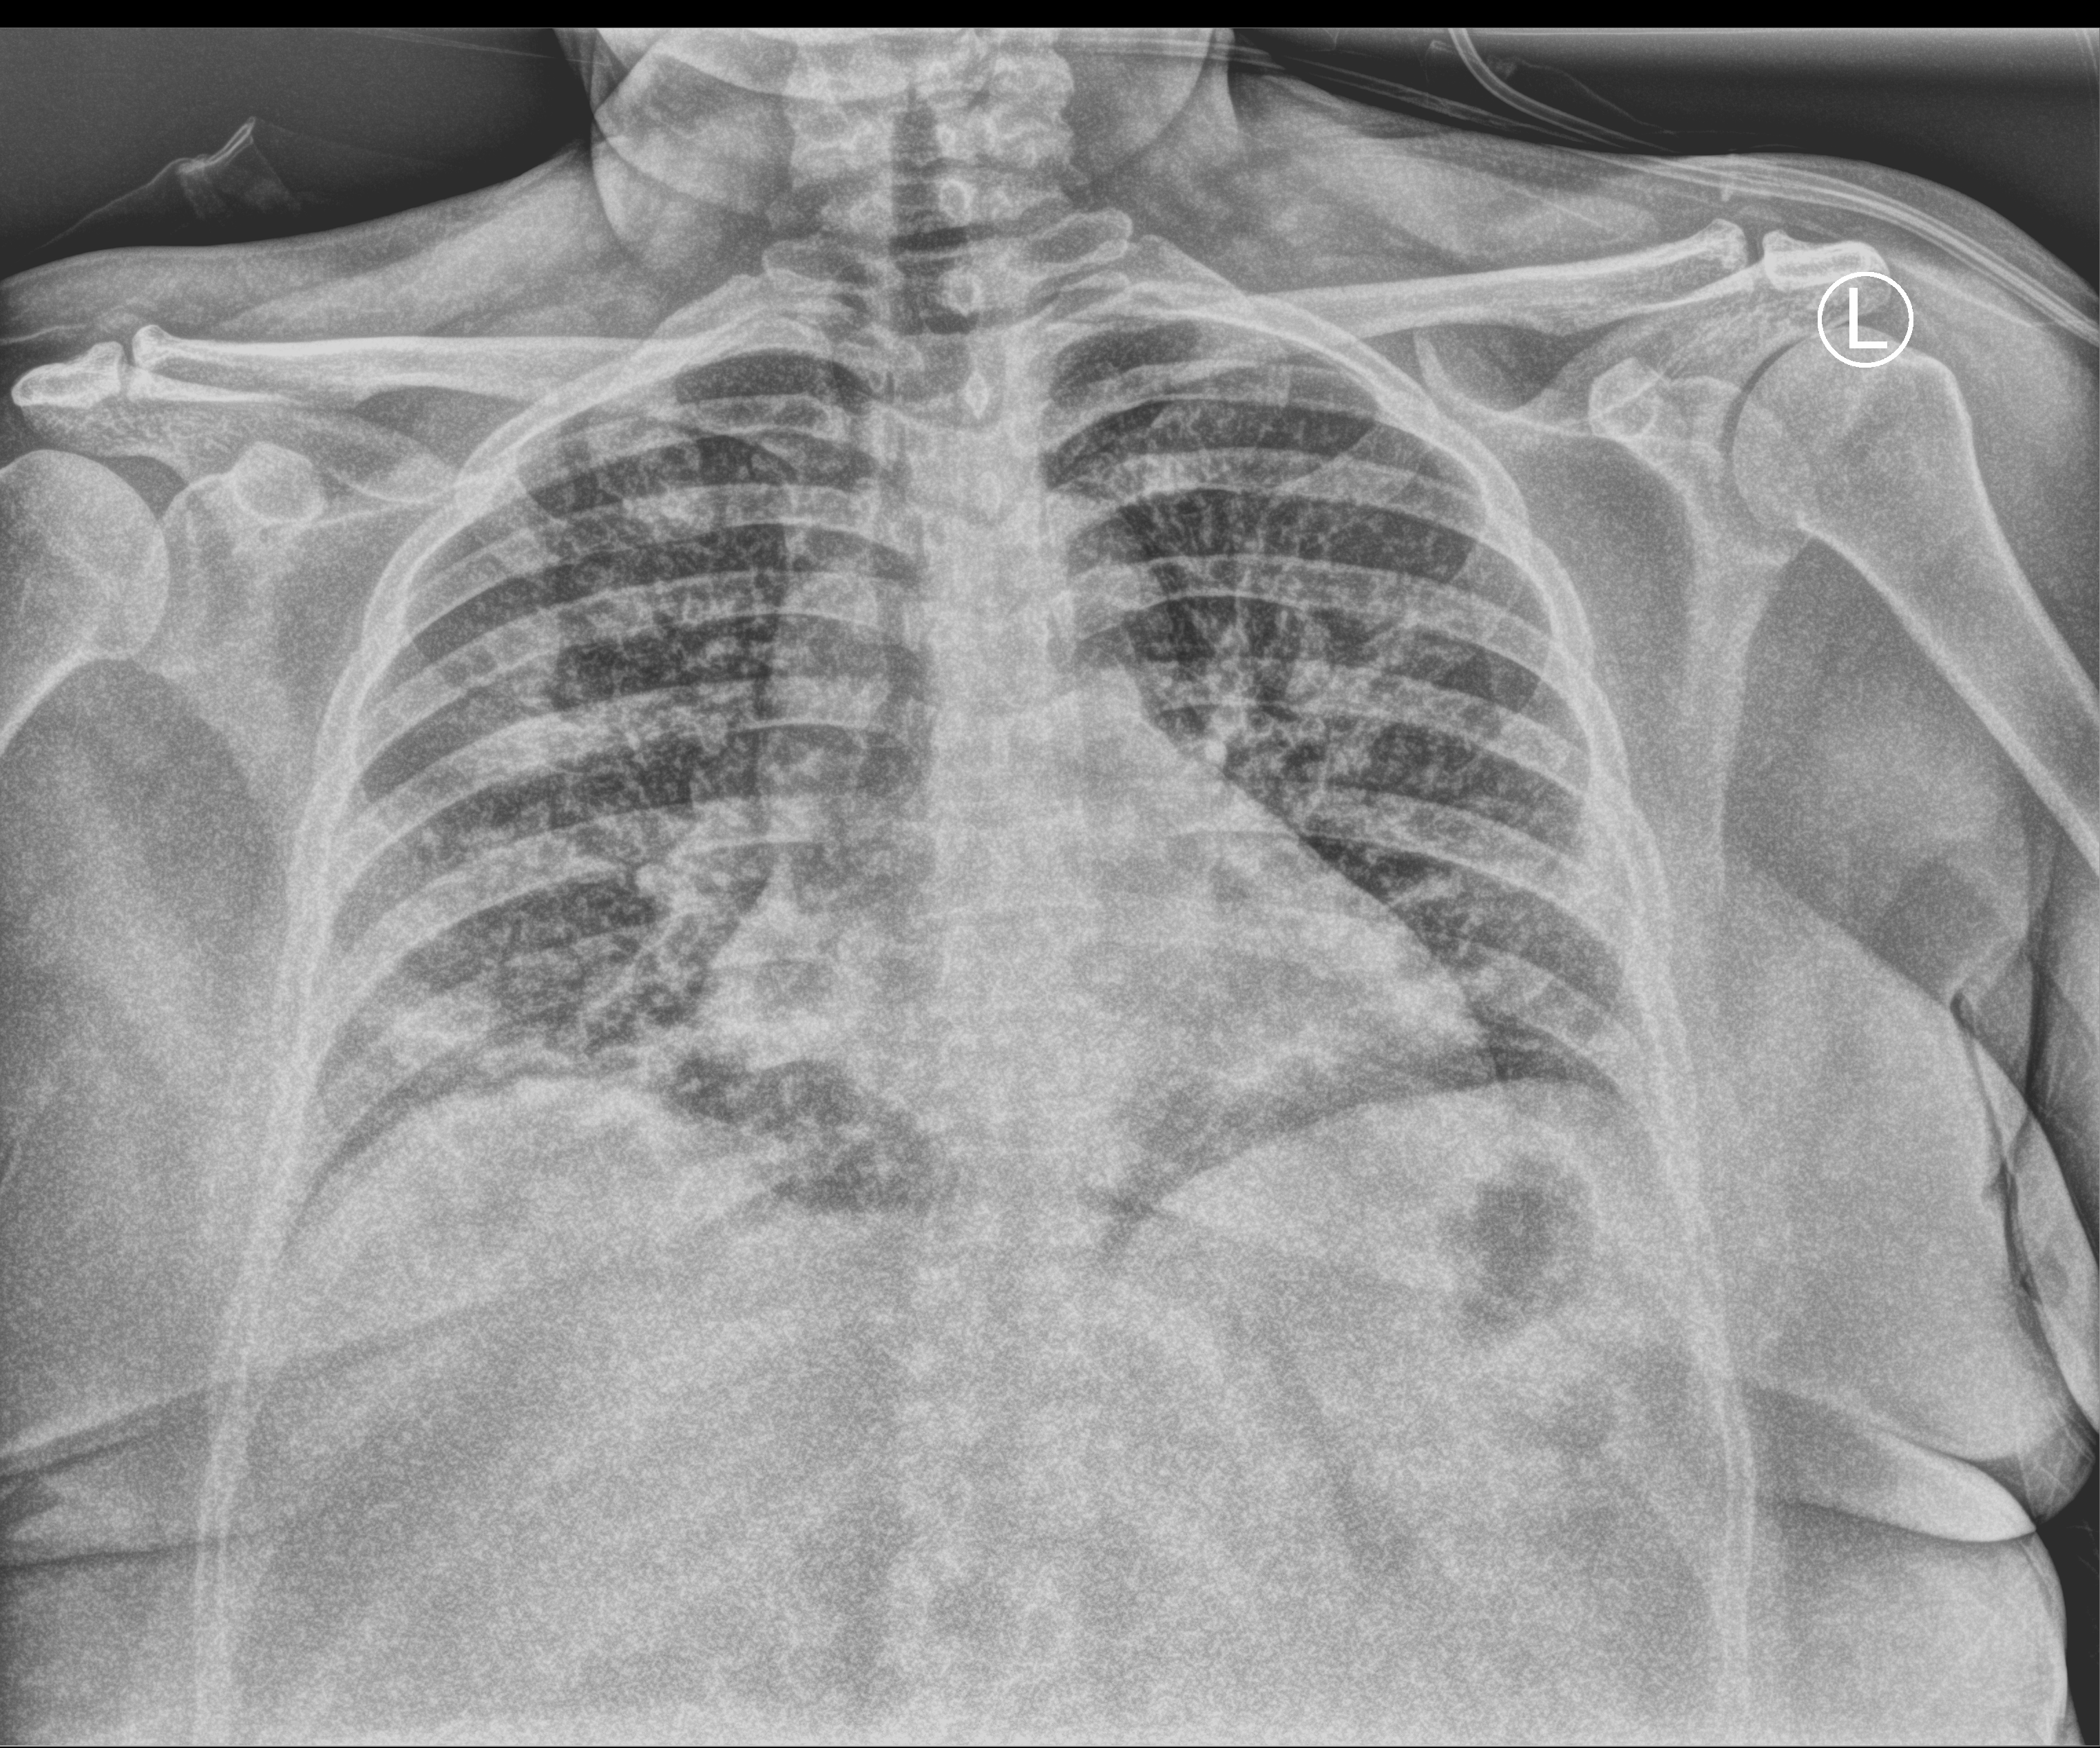
Chest X-ray (portable); anteroposterior (AP) projection. Patient hospitalised with COVID-19; female, aged 18–59 years.
Hospital-stay facts (about this admission, not read from this image; timing relative to this image not recorded):
- smoking status (admission record): never
- length of hospital stay: 6 days